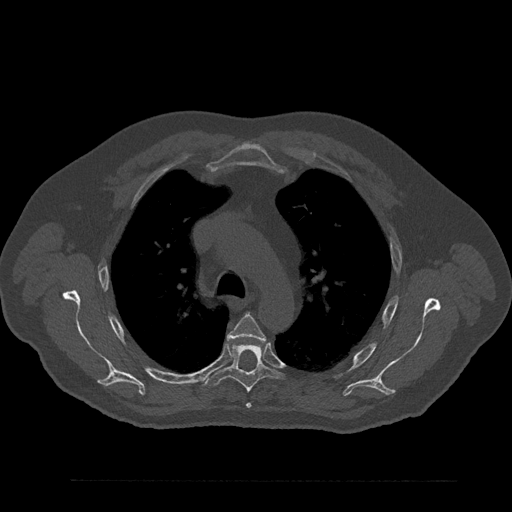
CT including the spine, one axial slice. Slice 613 of 797 in the series (ordered by position). Bone window (W 1800 / L 400 HU). 0.5 mm slice thickness. 512 × 512 image matrix, field of view 430 × 430 mm. Male patient, age 61 years. From the clinical record (not read from this slice): primary cancer: prostate.
Structures marked on this image (semi-automatic segmentation, software-assisted and operator-edited):
- T4 vertebra: bounding box (x1, y1, x2, y2) in pixels: (227, 314, 266, 408)
- T5 vertebra: (204, 341, 284, 393)